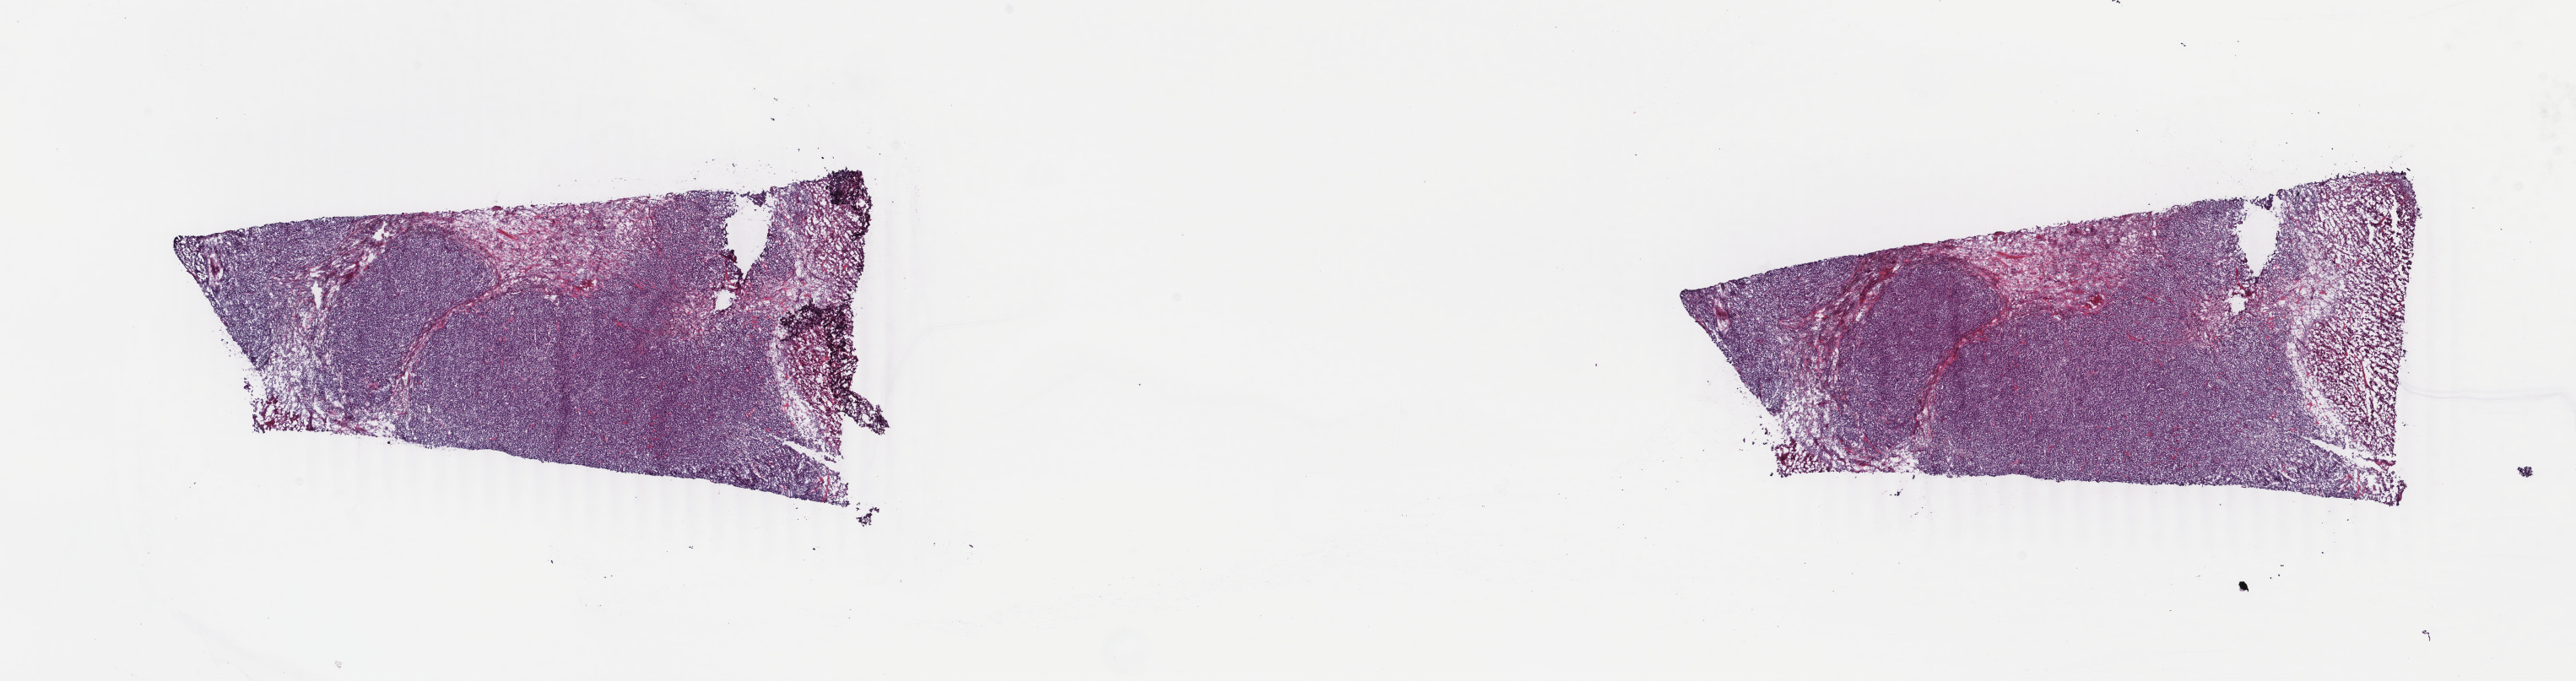
Whole-slide histology image, H&E-stained — whole scanned area (about 24.3 x 6.4 mm) shown as a low-resolution overview. Frozen section. Metastatic tumour sample, sampled site: connective, subcutaneous and other soft tissues of thorax. Male patient; age at initial diagnosis 45 years. Slide review estimates, as recorded: tumour cells 100%, tumour nuclei 95%, normal cells 0%, stromal cells 0%, necrosis 0%. Infiltration values recorded for this section: lymphocyte infiltration 0%, monocyte infiltration 0%, neutrophil infiltration 0%.
This section: metastatic tumour tissue. Patient diagnosis: Malignant melanoma, NOS.